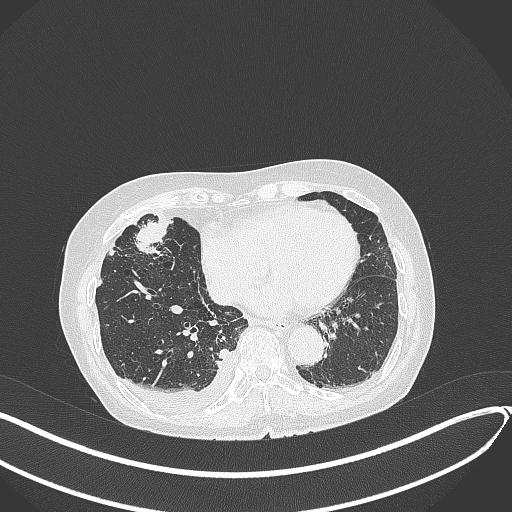
Chest CT, one axial slice. Slice 129 of 418 in the series (ordered by position). Reconstruction kernel B70f. Lung window (W 1500 / L -600 HU). 1 mm slice thickness. 512 × 512 image matrix, field of view 400 × 400 mm. Female patient, age 75 years. Case-level facts recorded for this patient, not image findings: clinical TNM (as recorded): T2a N3 M0.
Structures marked on this image (bounding box drawn by a radiologist):
- lung tumour (recorded histology: adenocarcinoma): bounding box <127,215,170,264> (left, top, right, bottom; pixels)